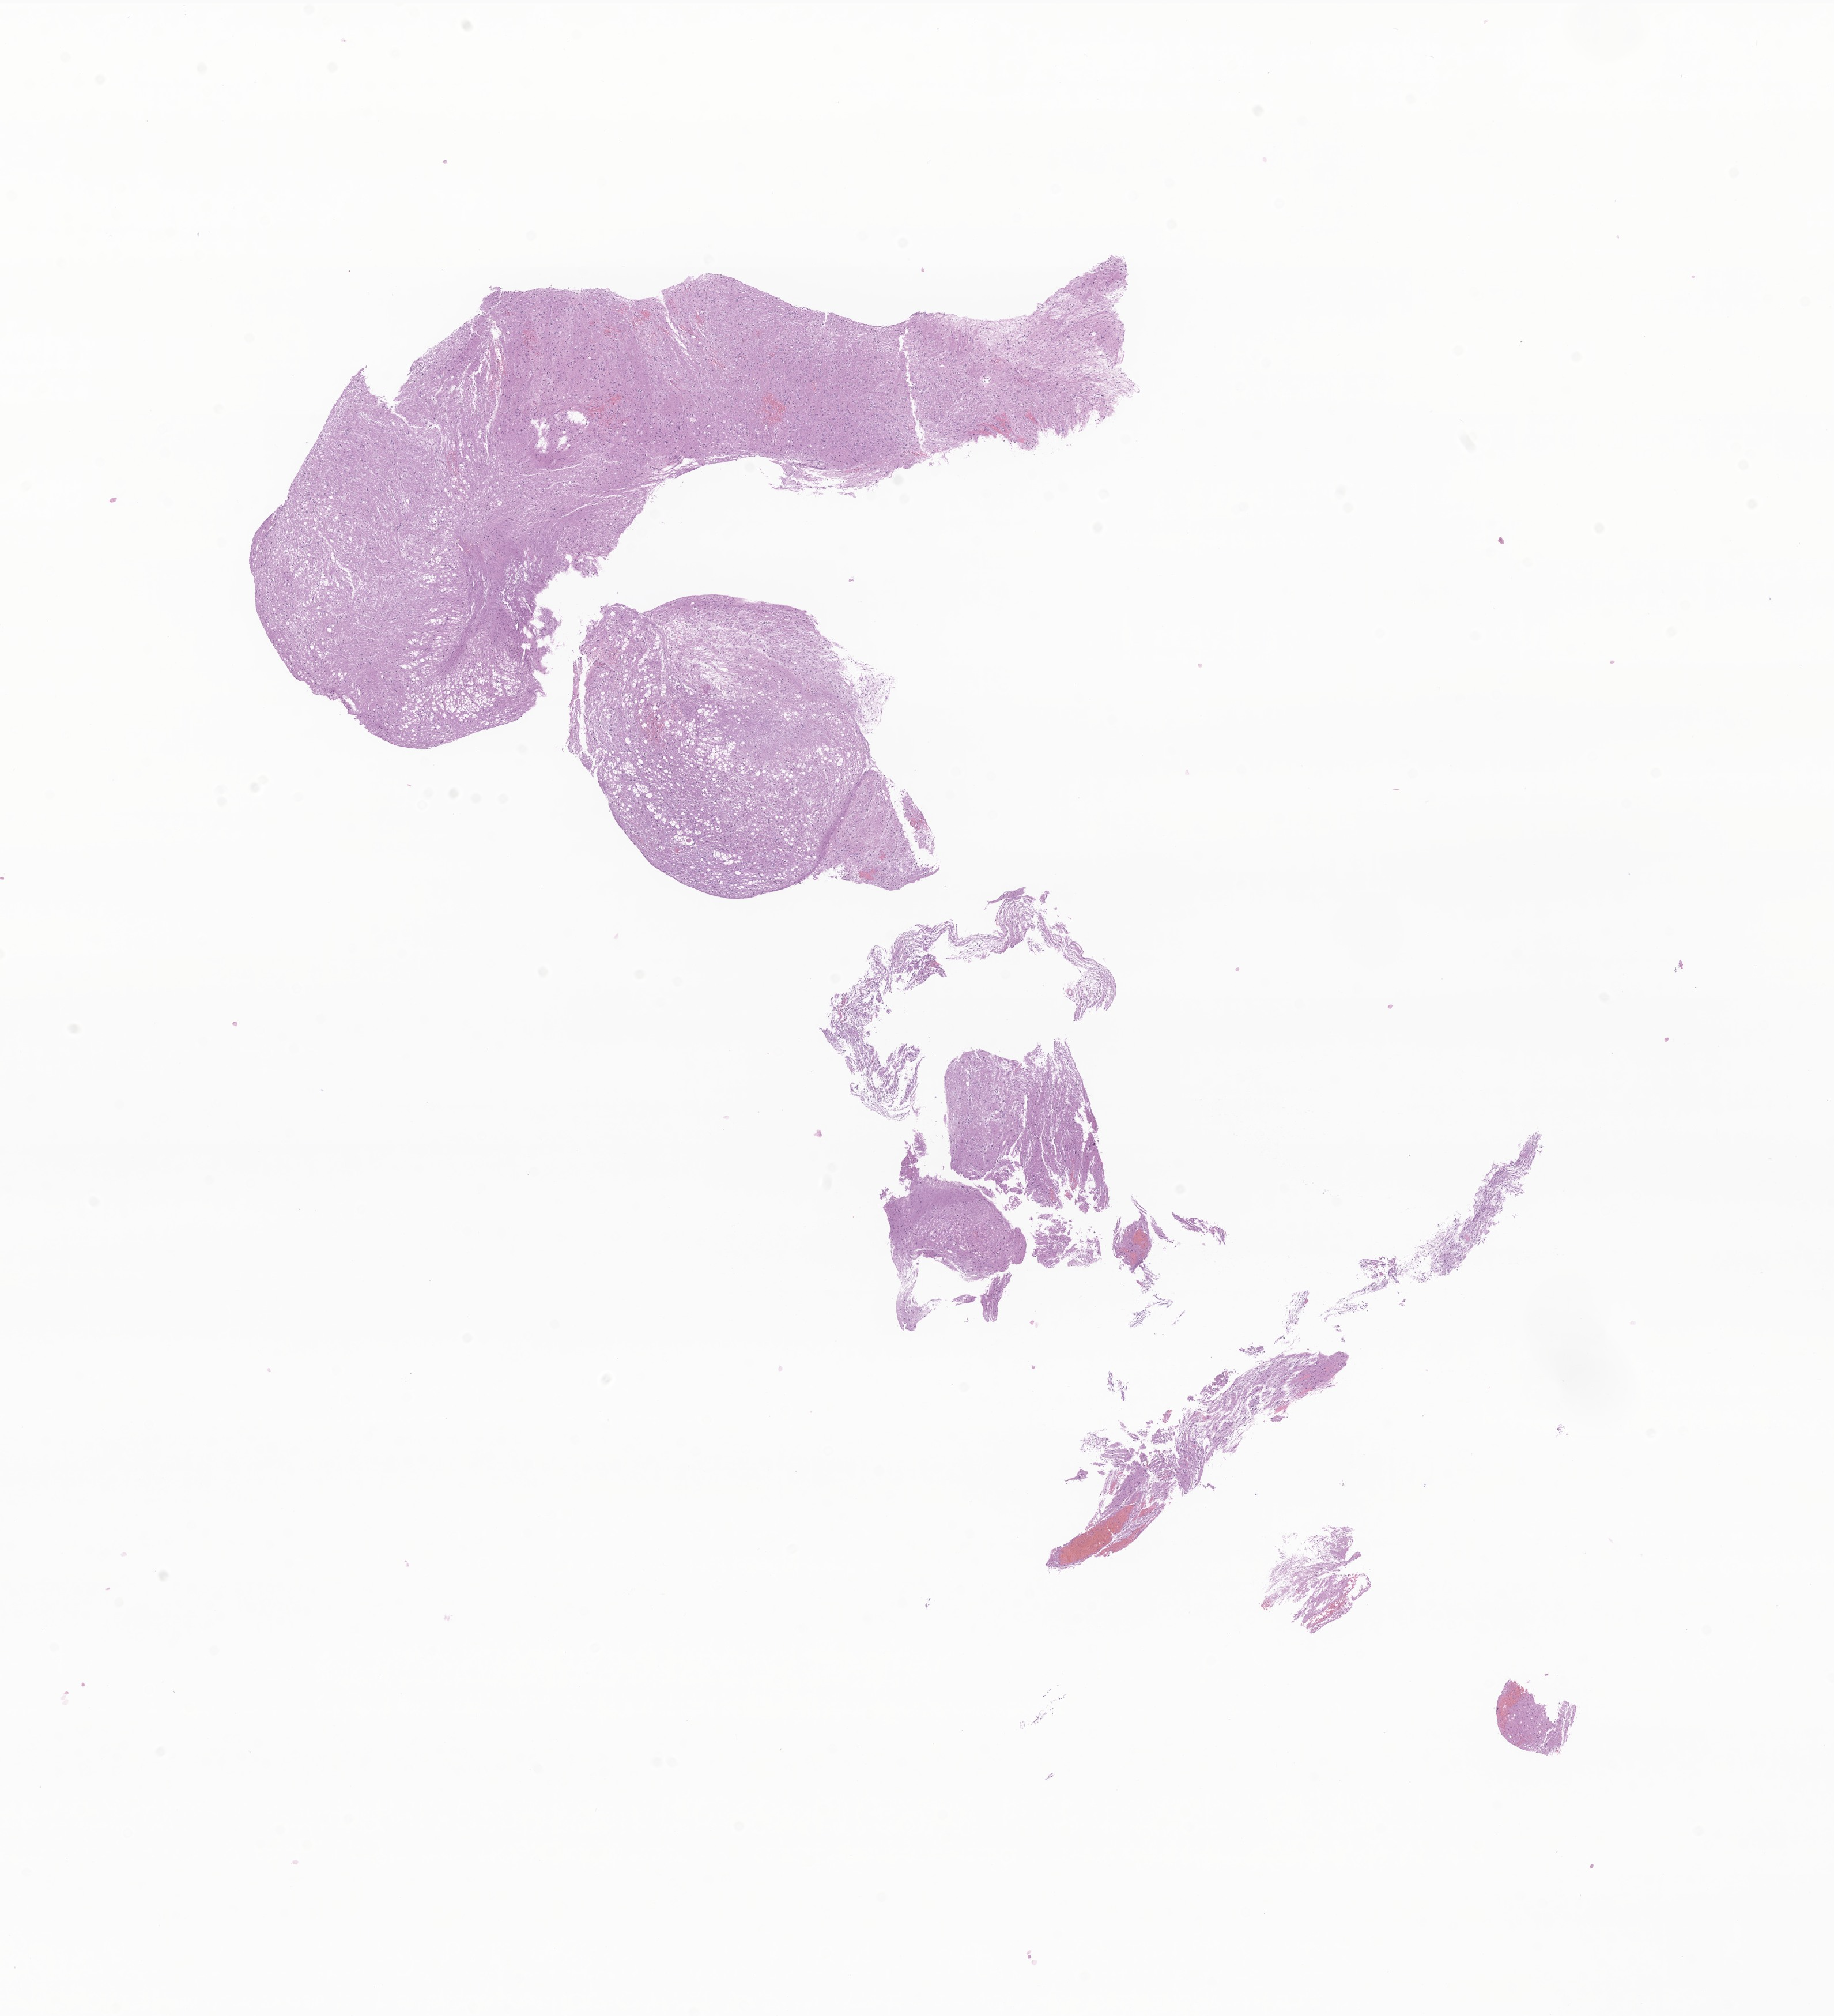
Haematoxylin and eosin whole-slide image of tumor tissue from the brain stem, shown as a low-resolution overview of the whole scanned area (about 13.4 x 14.7 mm). Formalin-fixed, paraffin-embedded (FFPE) tissue. Patient: male, age 72 months (6 years).
* diagnosis (ICD-O-3 morphology term): Glioma, malignant